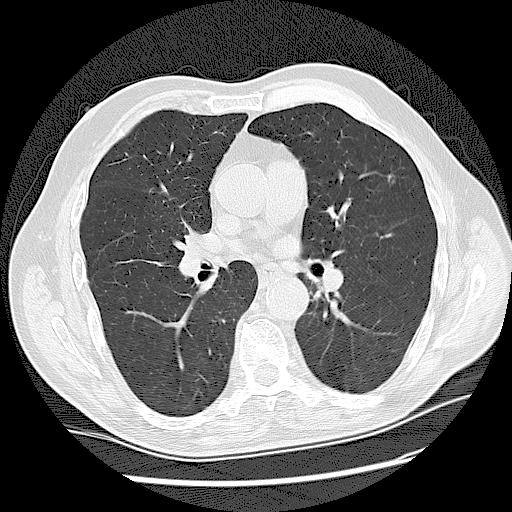
Low-dose screening chest CT, one axial slice; slice 85 of 159 in the series (ordered by position); 120 kVp; lung window (W 1500 / L -600 HU); 2.5 mm slice thickness; 512 × 512 image matrix, field of view 360 × 360 mm.
Structures marked on this image (outlined manually by an expert reader):
- lesion 1 (tumor, upper lobe of left lung): bounding box [x1, y1, x2, y2] px = [388, 175, 391, 179]